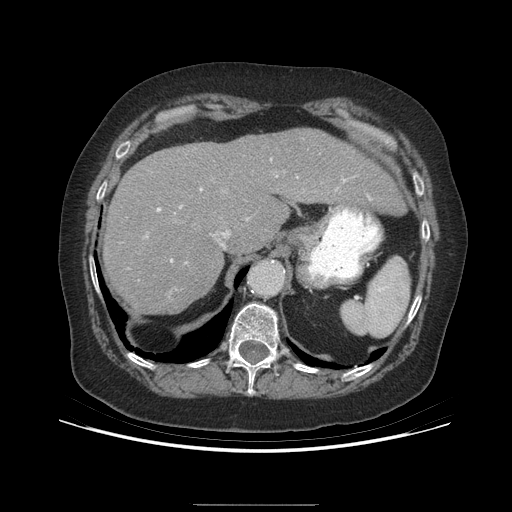
Contrast-enhanced abdominal CT (liver protocol), one axial slice; position 168 of 192 along the scan axis; reconstruction kernel STANDARD; 140 kVp; soft-tissue window (W 400 / L 40 HU); 512 × 512 image matrix, field of view 400 × 400 mm. From the clinical record (not read from this slice): diagnosis: hepatocellular carcinoma (patient treated with transarterial chemoembolisation; whether this scan precedes or follows treatment is not stated here); TNM stage (as recorded): Stage-I; Child-Pugh class: A; tumour differentiation: moderately differentiated; tumour nodularity: uninodular.
Outlined on this slice (semi-automatic segmentation, software-assisted and operator-edited):
- liver parenchyma outside the tumour (the mass and vessels are separate outlines, so this box may not span the whole liver): bounding box [x1, y1, x2, y2] px = [102, 128, 404, 314]
- liver vessels: [157, 180, 345, 262]